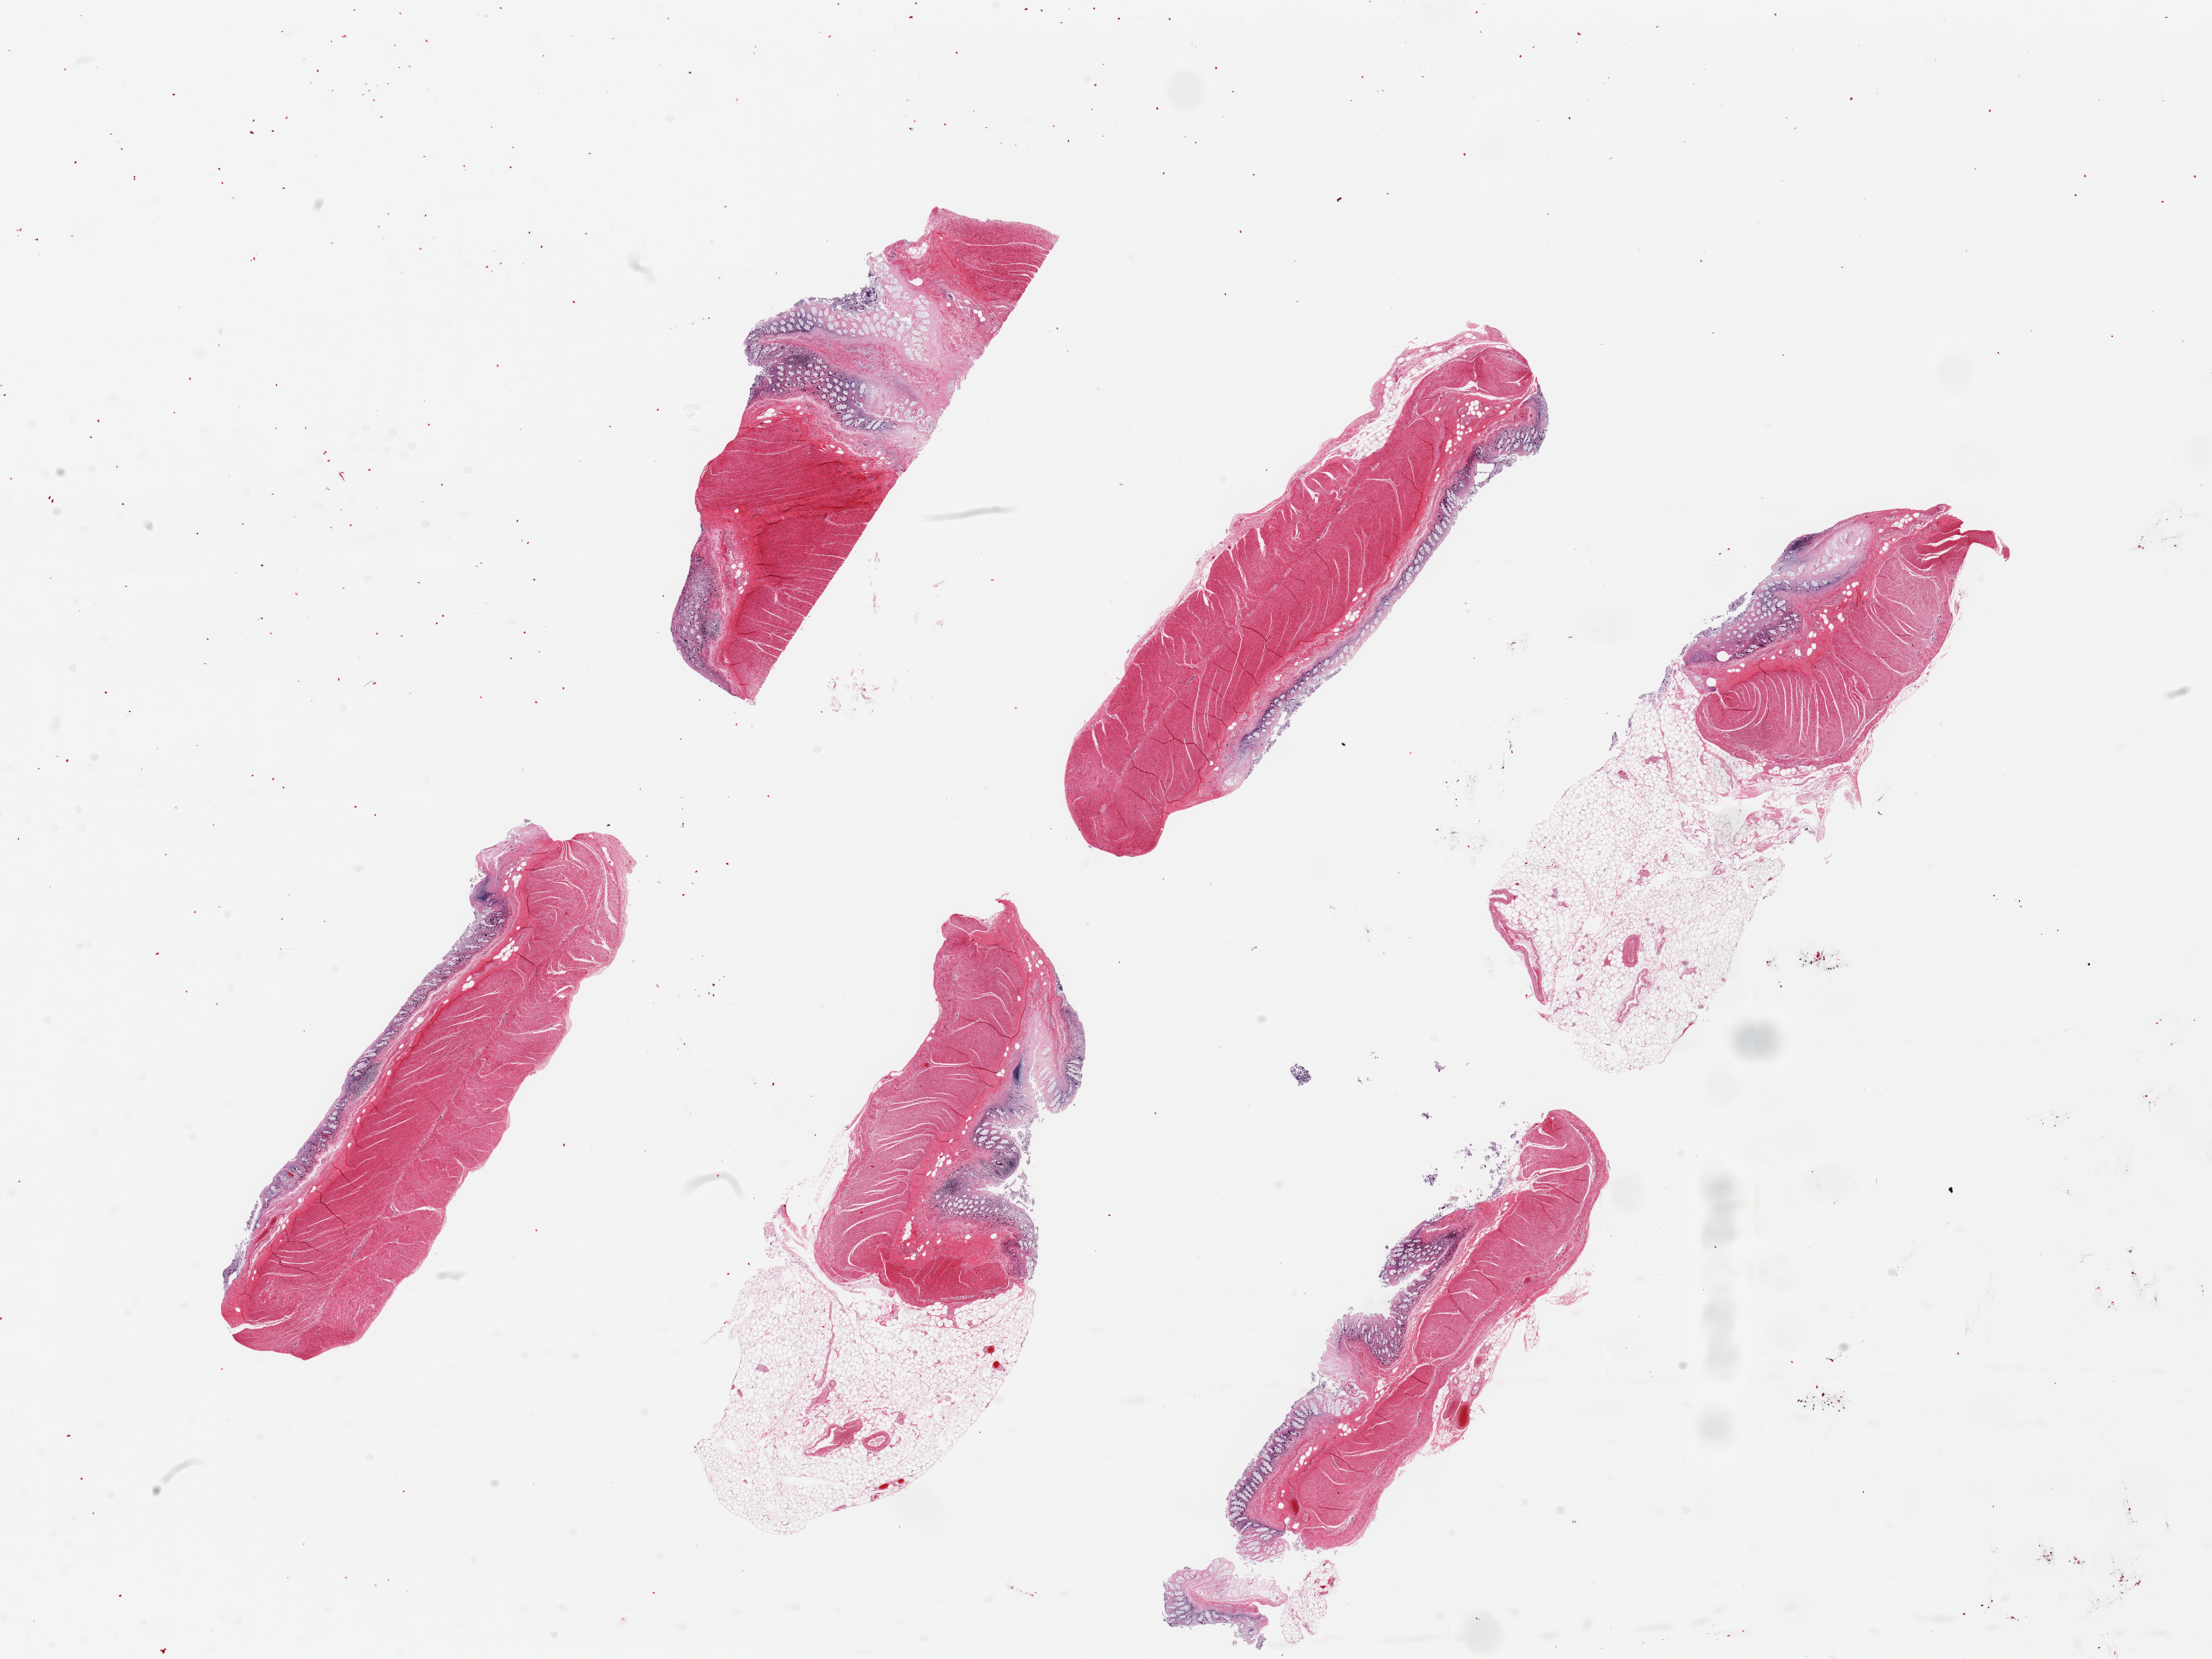
Whole-slide image, H&E stain — low-resolution overview of the scanned area, about 28.5 x 21.4 mm. Donor sex: male.
Specimen: PAXgene-fixed, paraffin-embedded tissue; sampled site (target tissue): sigmoid colon; donor tissue sample.